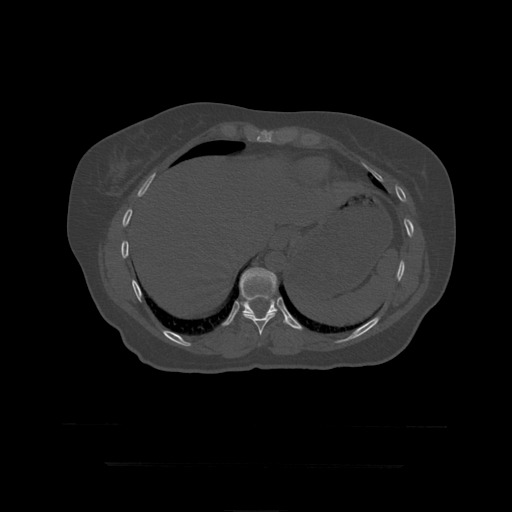
CT including the spine, one axial slice; reconstruction kernel STANDARD; 120 kVp; bone window (W 1800 / L 400 HU); 1.25 mm slice thickness; 512 × 512 image matrix, field of view 450 × 450 mm. Patient age 41 years. Case-level facts recorded for this patient, not image findings: primary cancer: breast.
Outlined on this slice (semi-automatically segmented with operator editing):
- T10 vertebra: box from (x=243, y=311) to (x=278, y=336) px
- T11 vertebra: (x=240, y=268)–(x=287, y=324)